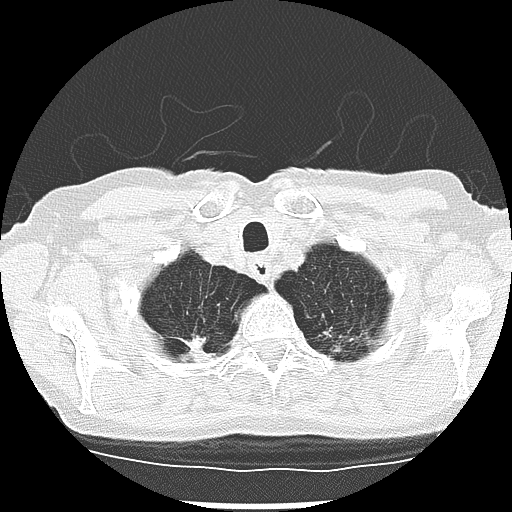
Low-dose screening chest CT, one axial slice; reconstruction kernel LUNG; lung window (W 1500 / L -600 HU); 2.5 mm slice thickness; 512 × 512 image matrix, field of view 300 × 300 mm.
Structures marked on this image (manually delineated by an expert):
- lesion 2 (tumor, upper lobe of right lung): bounding box (x1, y1, x2, y2) in pixels: (186, 335, 205, 353)